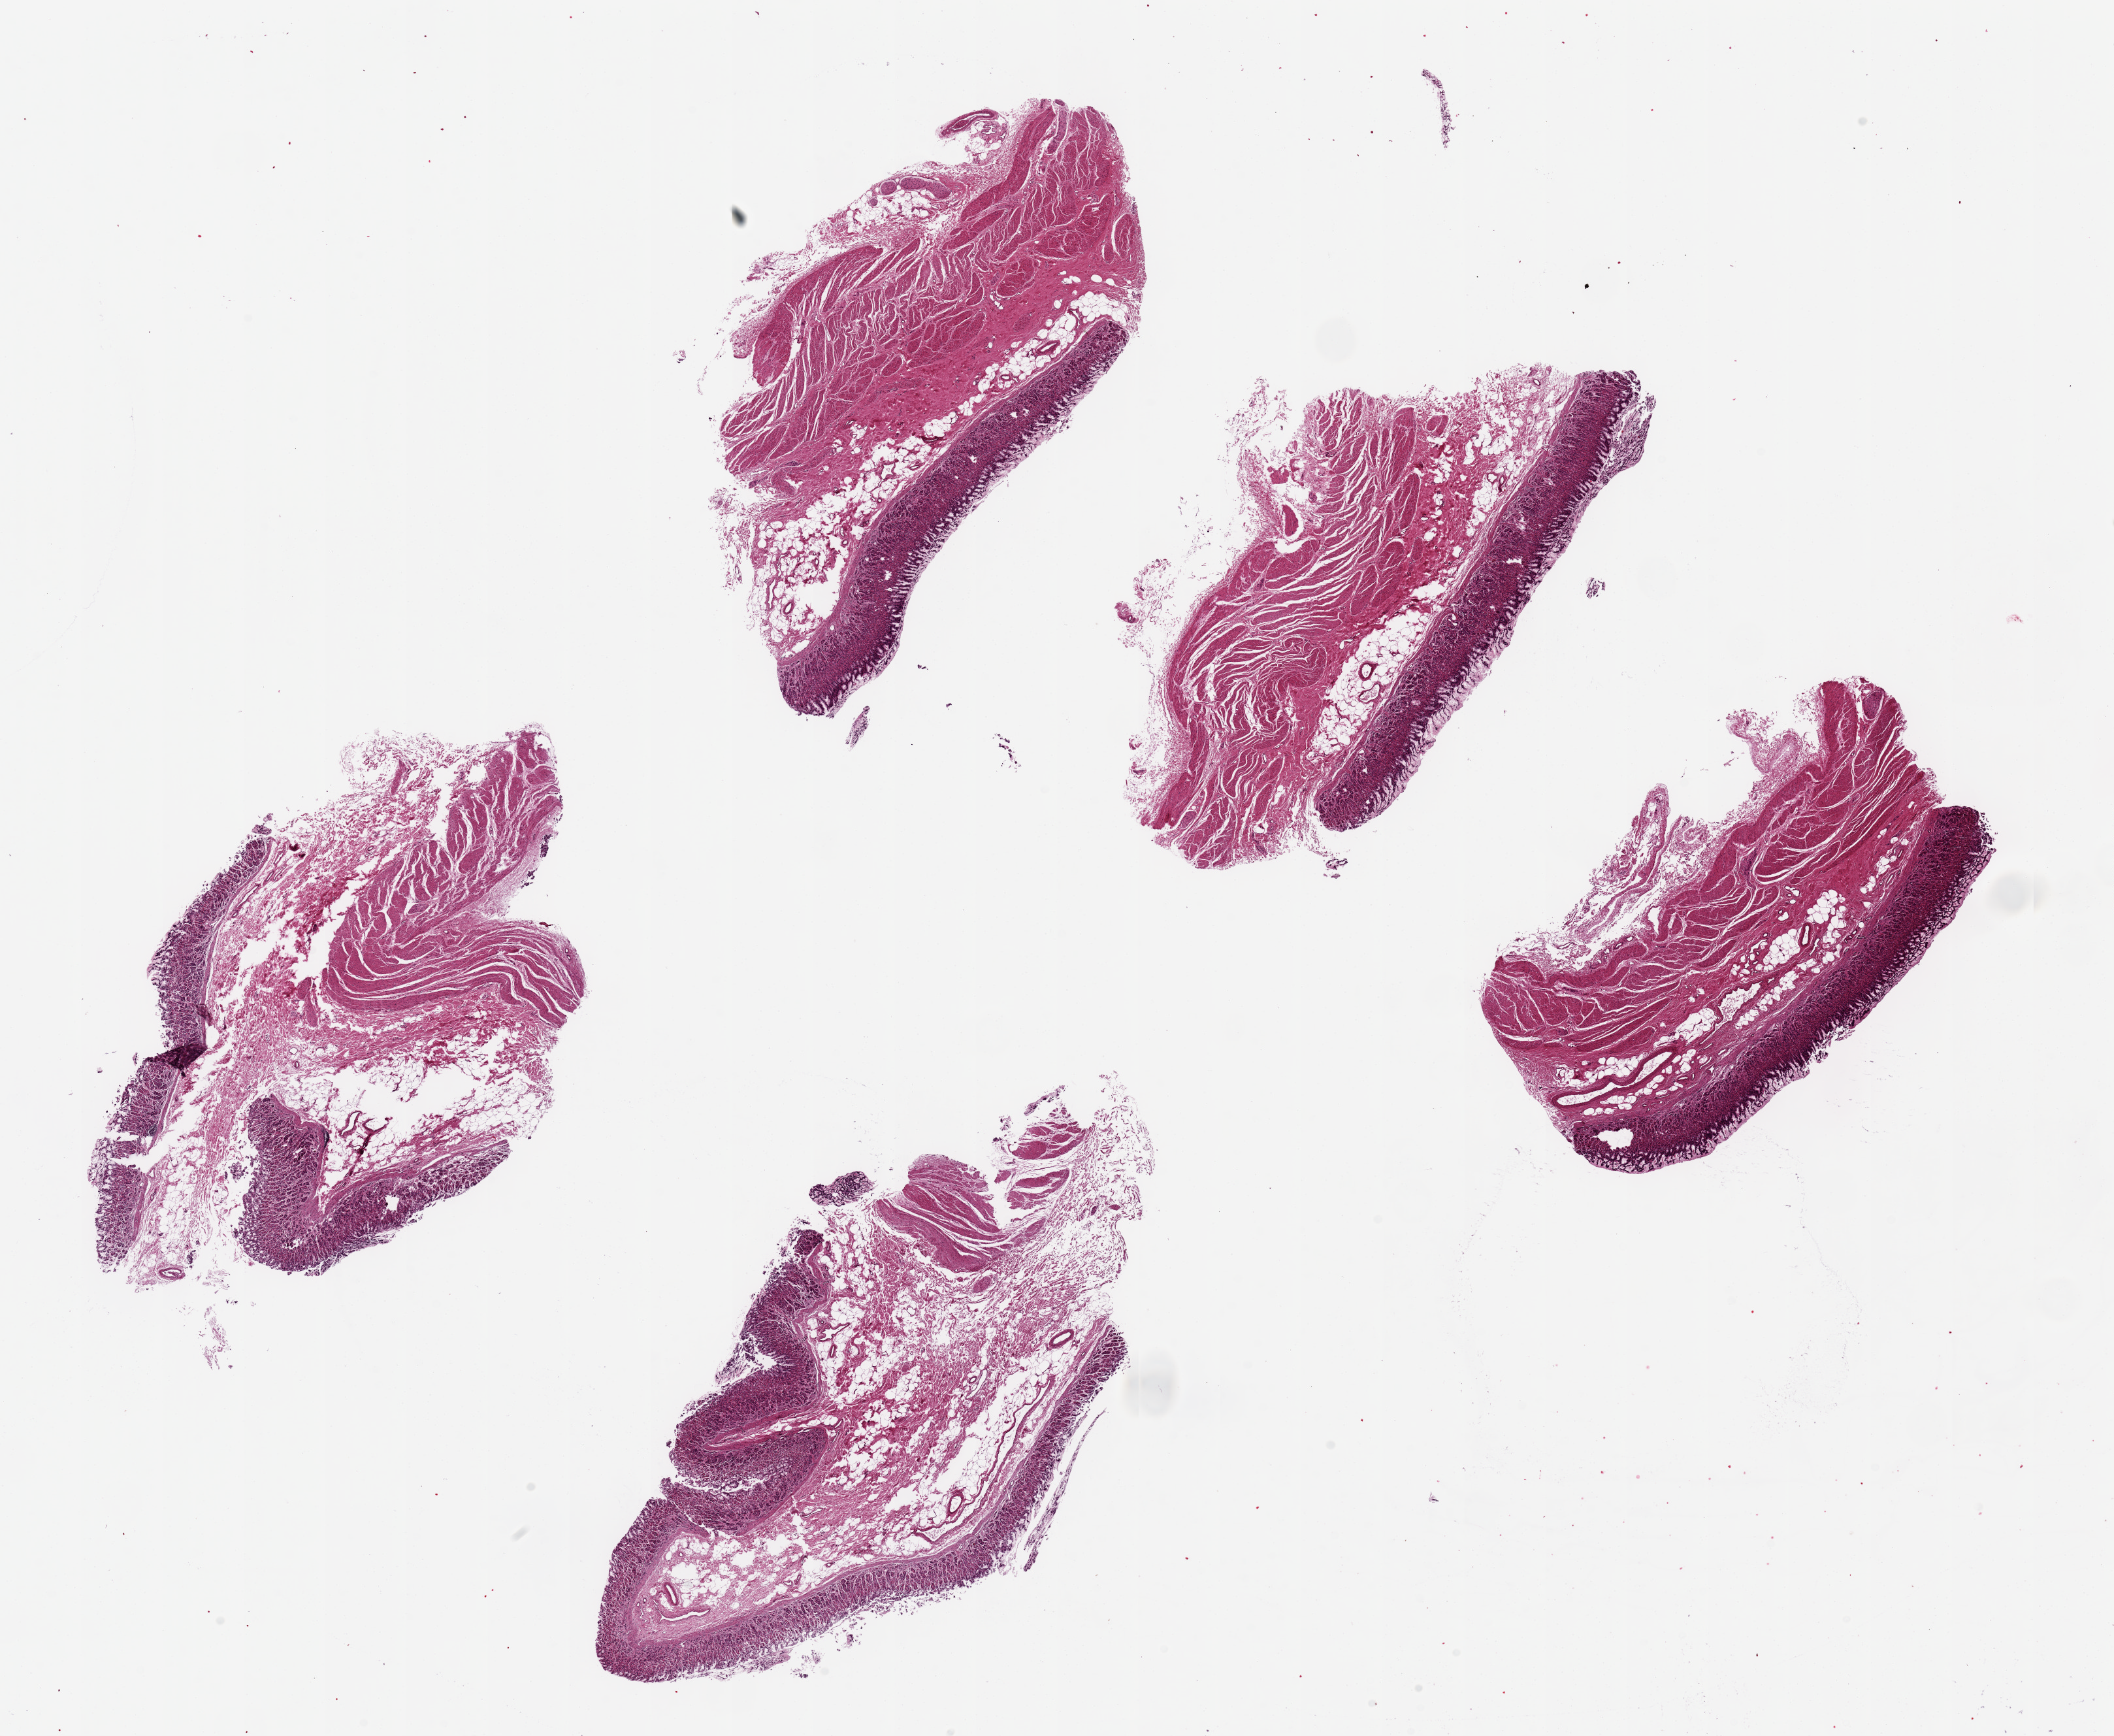
Haematoxylin and eosin whole-slide image — whole scanned area (about 25.6 x 21.0 mm) shown as a low-resolution overview; PAXgene-fixed paraffin-embedded (PFPE) section; target tissue: stomach; donor tissue sample. Male donor.
• review note (as recorded): 5 ~6.5x3.5mm pieces; mucosa exceptionally well-preserved and ~15-20% of thickness